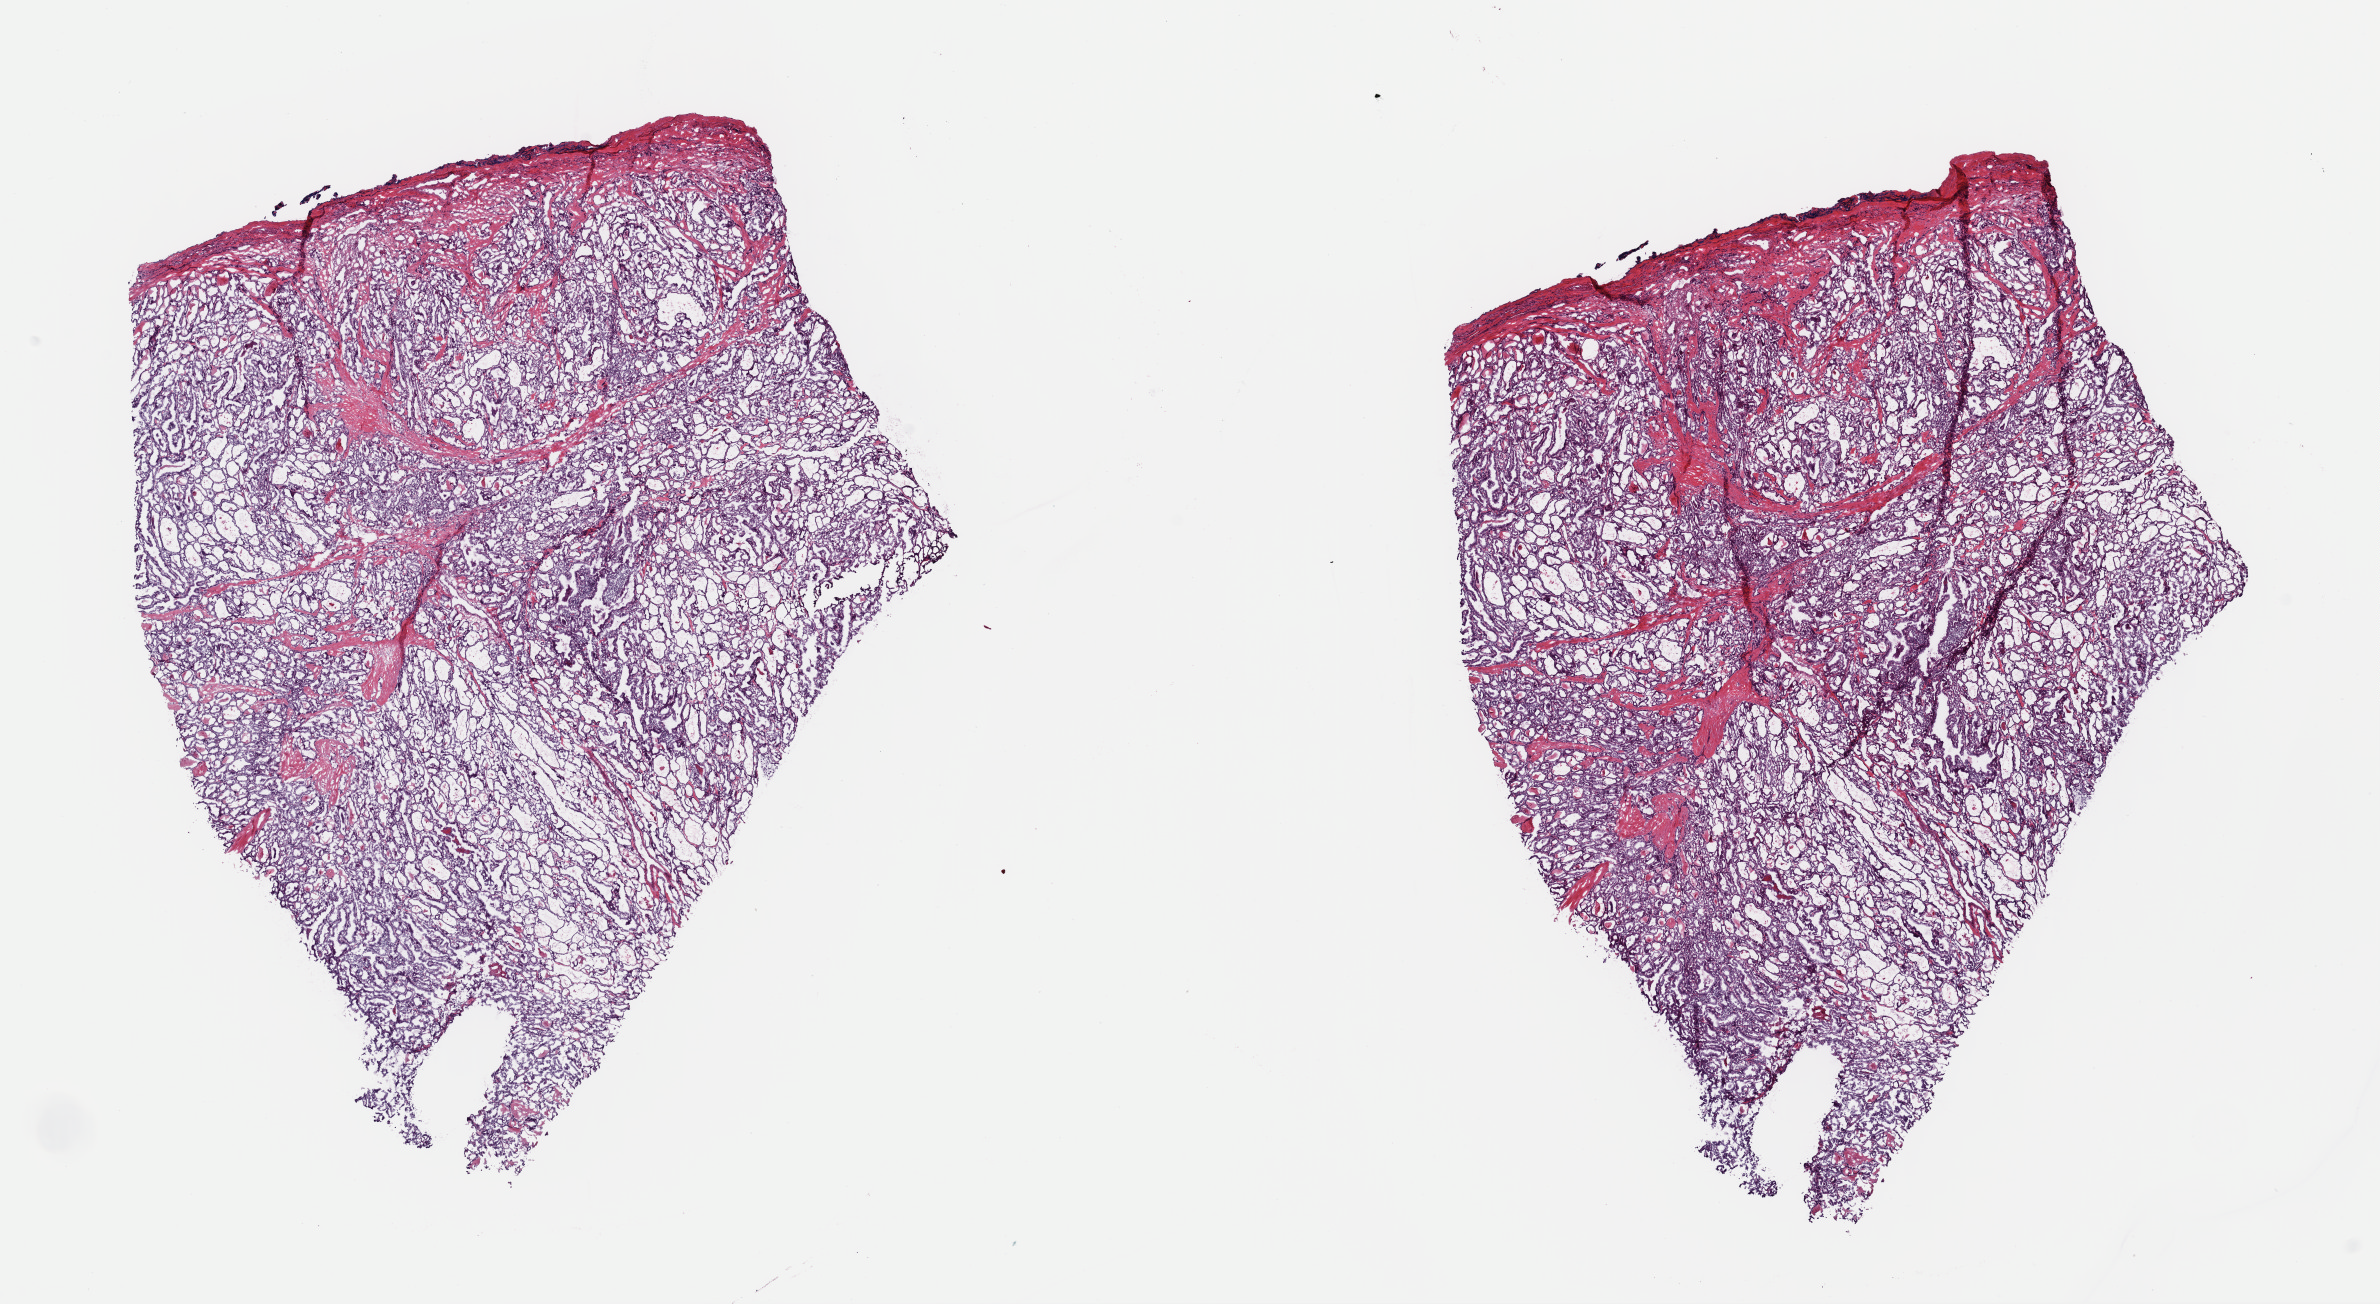
Whole-slide histology image, H&E, shown as a low-resolution overview of the whole scanned area (about 18.8 x 10.3 mm, from a 40x scan). Frozen section from the top of the tissue portion. Primary tumour sample from the thyroid. Patient: male, age at initial diagnosis 37 years. Slide review estimates, as recorded: tumour cells 90%, tumour nuclei 95%, normal cells 0%, stromal cells 10%, necrosis 0%. Inflammatory infiltration, as recorded: lymphocyte infiltration 1%, monocyte infiltration 0%, neutrophil infiltration 0%.
AJCC pathologic stage: I (6th edition). TNM: T3 N1a M0. Laterality: bilateral. Lymph nodes positive (case pathology): 4 of 5 examined. Diagnosis: Papillary carcinoma, follicular variant (thyroid gland).